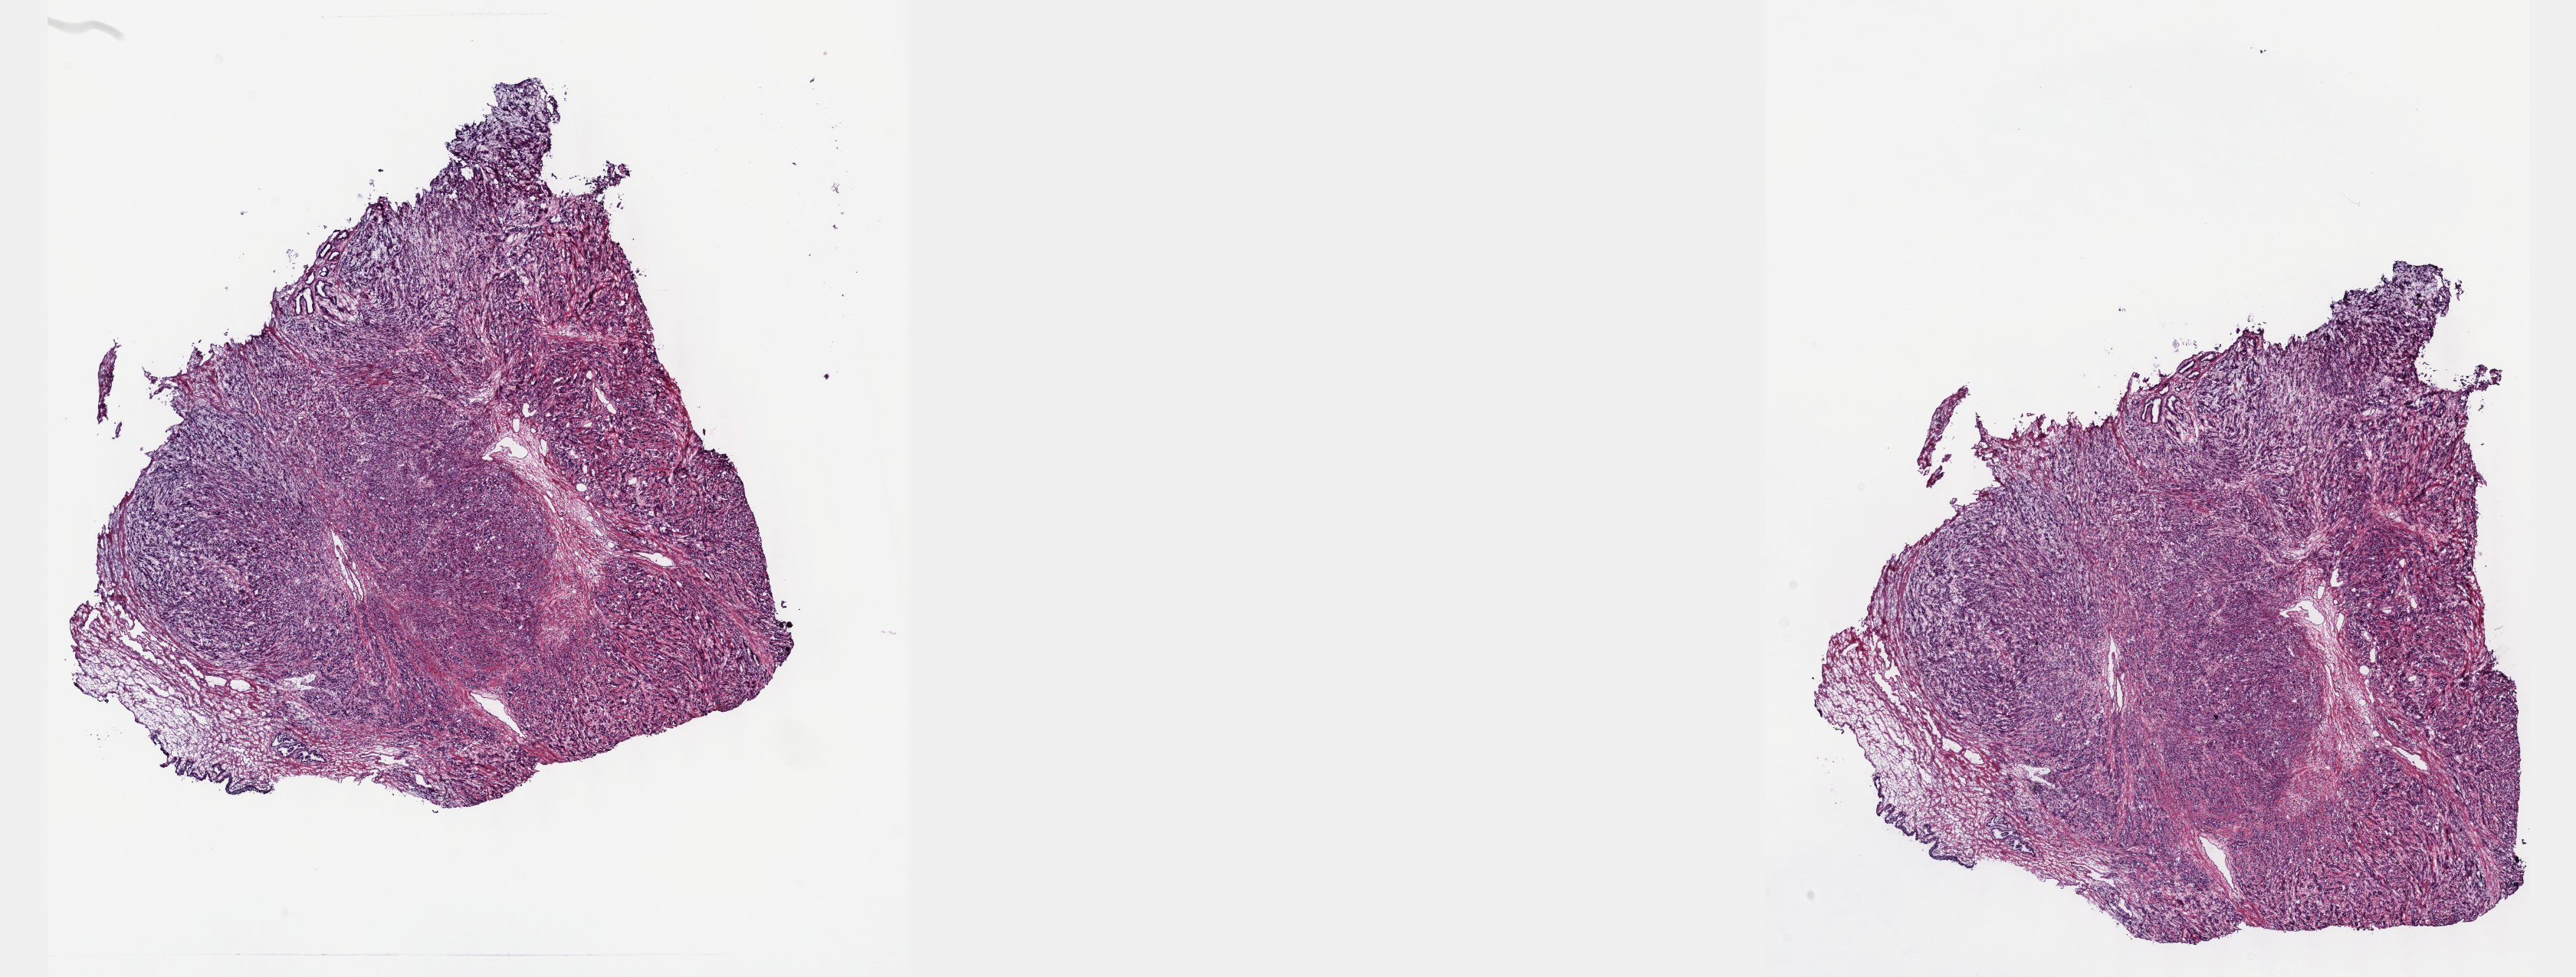
Whole-slide histology image, Hematoxylin and eosin (H&E) stained — whole scanned area (about 27.2 x 10.3 mm) shown as a low-resolution overview, frozen section, primary tumour sample from the prostate. Patient: male, age at initial diagnosis 64 years. Gleason score: 9 (4+5). Pathologist review of this section (percent, as recorded): tumour cells 90%, tumour nuclei 90%, normal cells 0%, stromal cells 5%, necrosis 5%. Inflammatory infiltration, as recorded: lymphocyte infiltration 40%, monocyte infiltration 20%, neutrophil infiltration 20%.
* pathologic diagnosis: Adenocarcinoma, NOS (prostate gland)